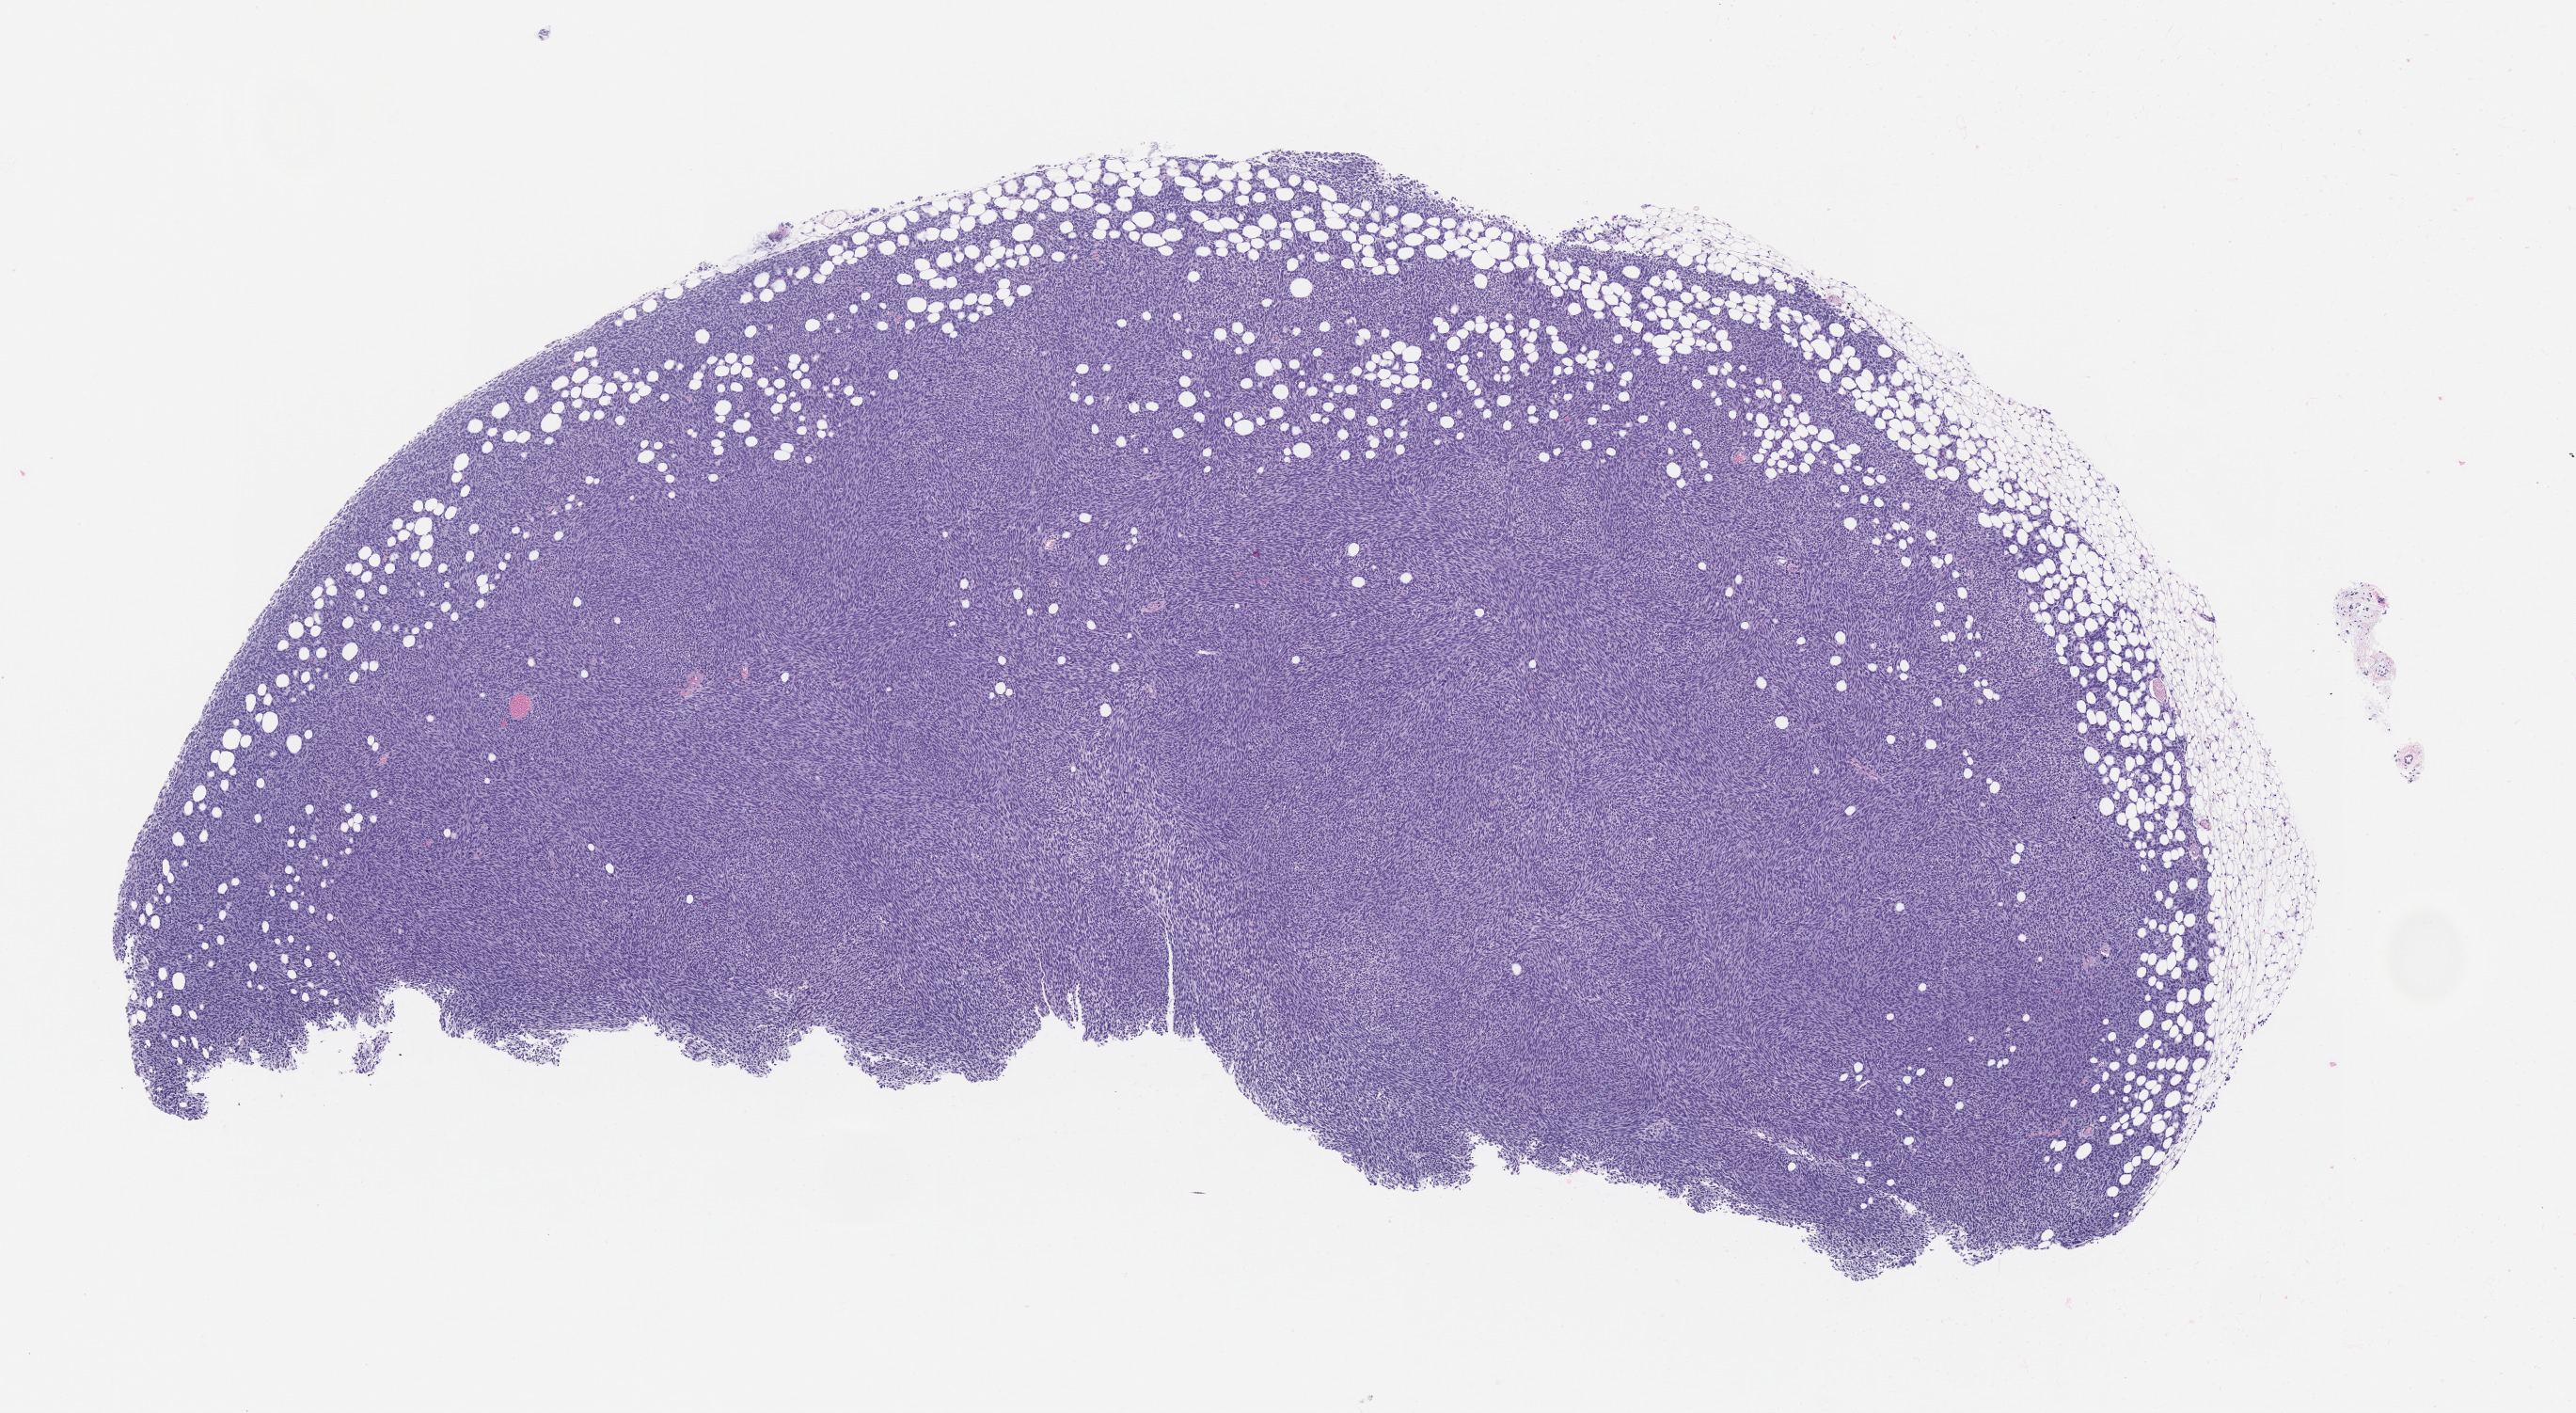
Whole-slide image, haematoxylin and eosin: patient-derived xenograft (human tumor grown in a mouse), passage 1 — shown as a low-resolution overview of the whole scanned area (about 11.0 x 6.0 mm); FFPE section; tumor site category: musculoskeletal.
- originating patient diagnosis: Synovial Sarcoma